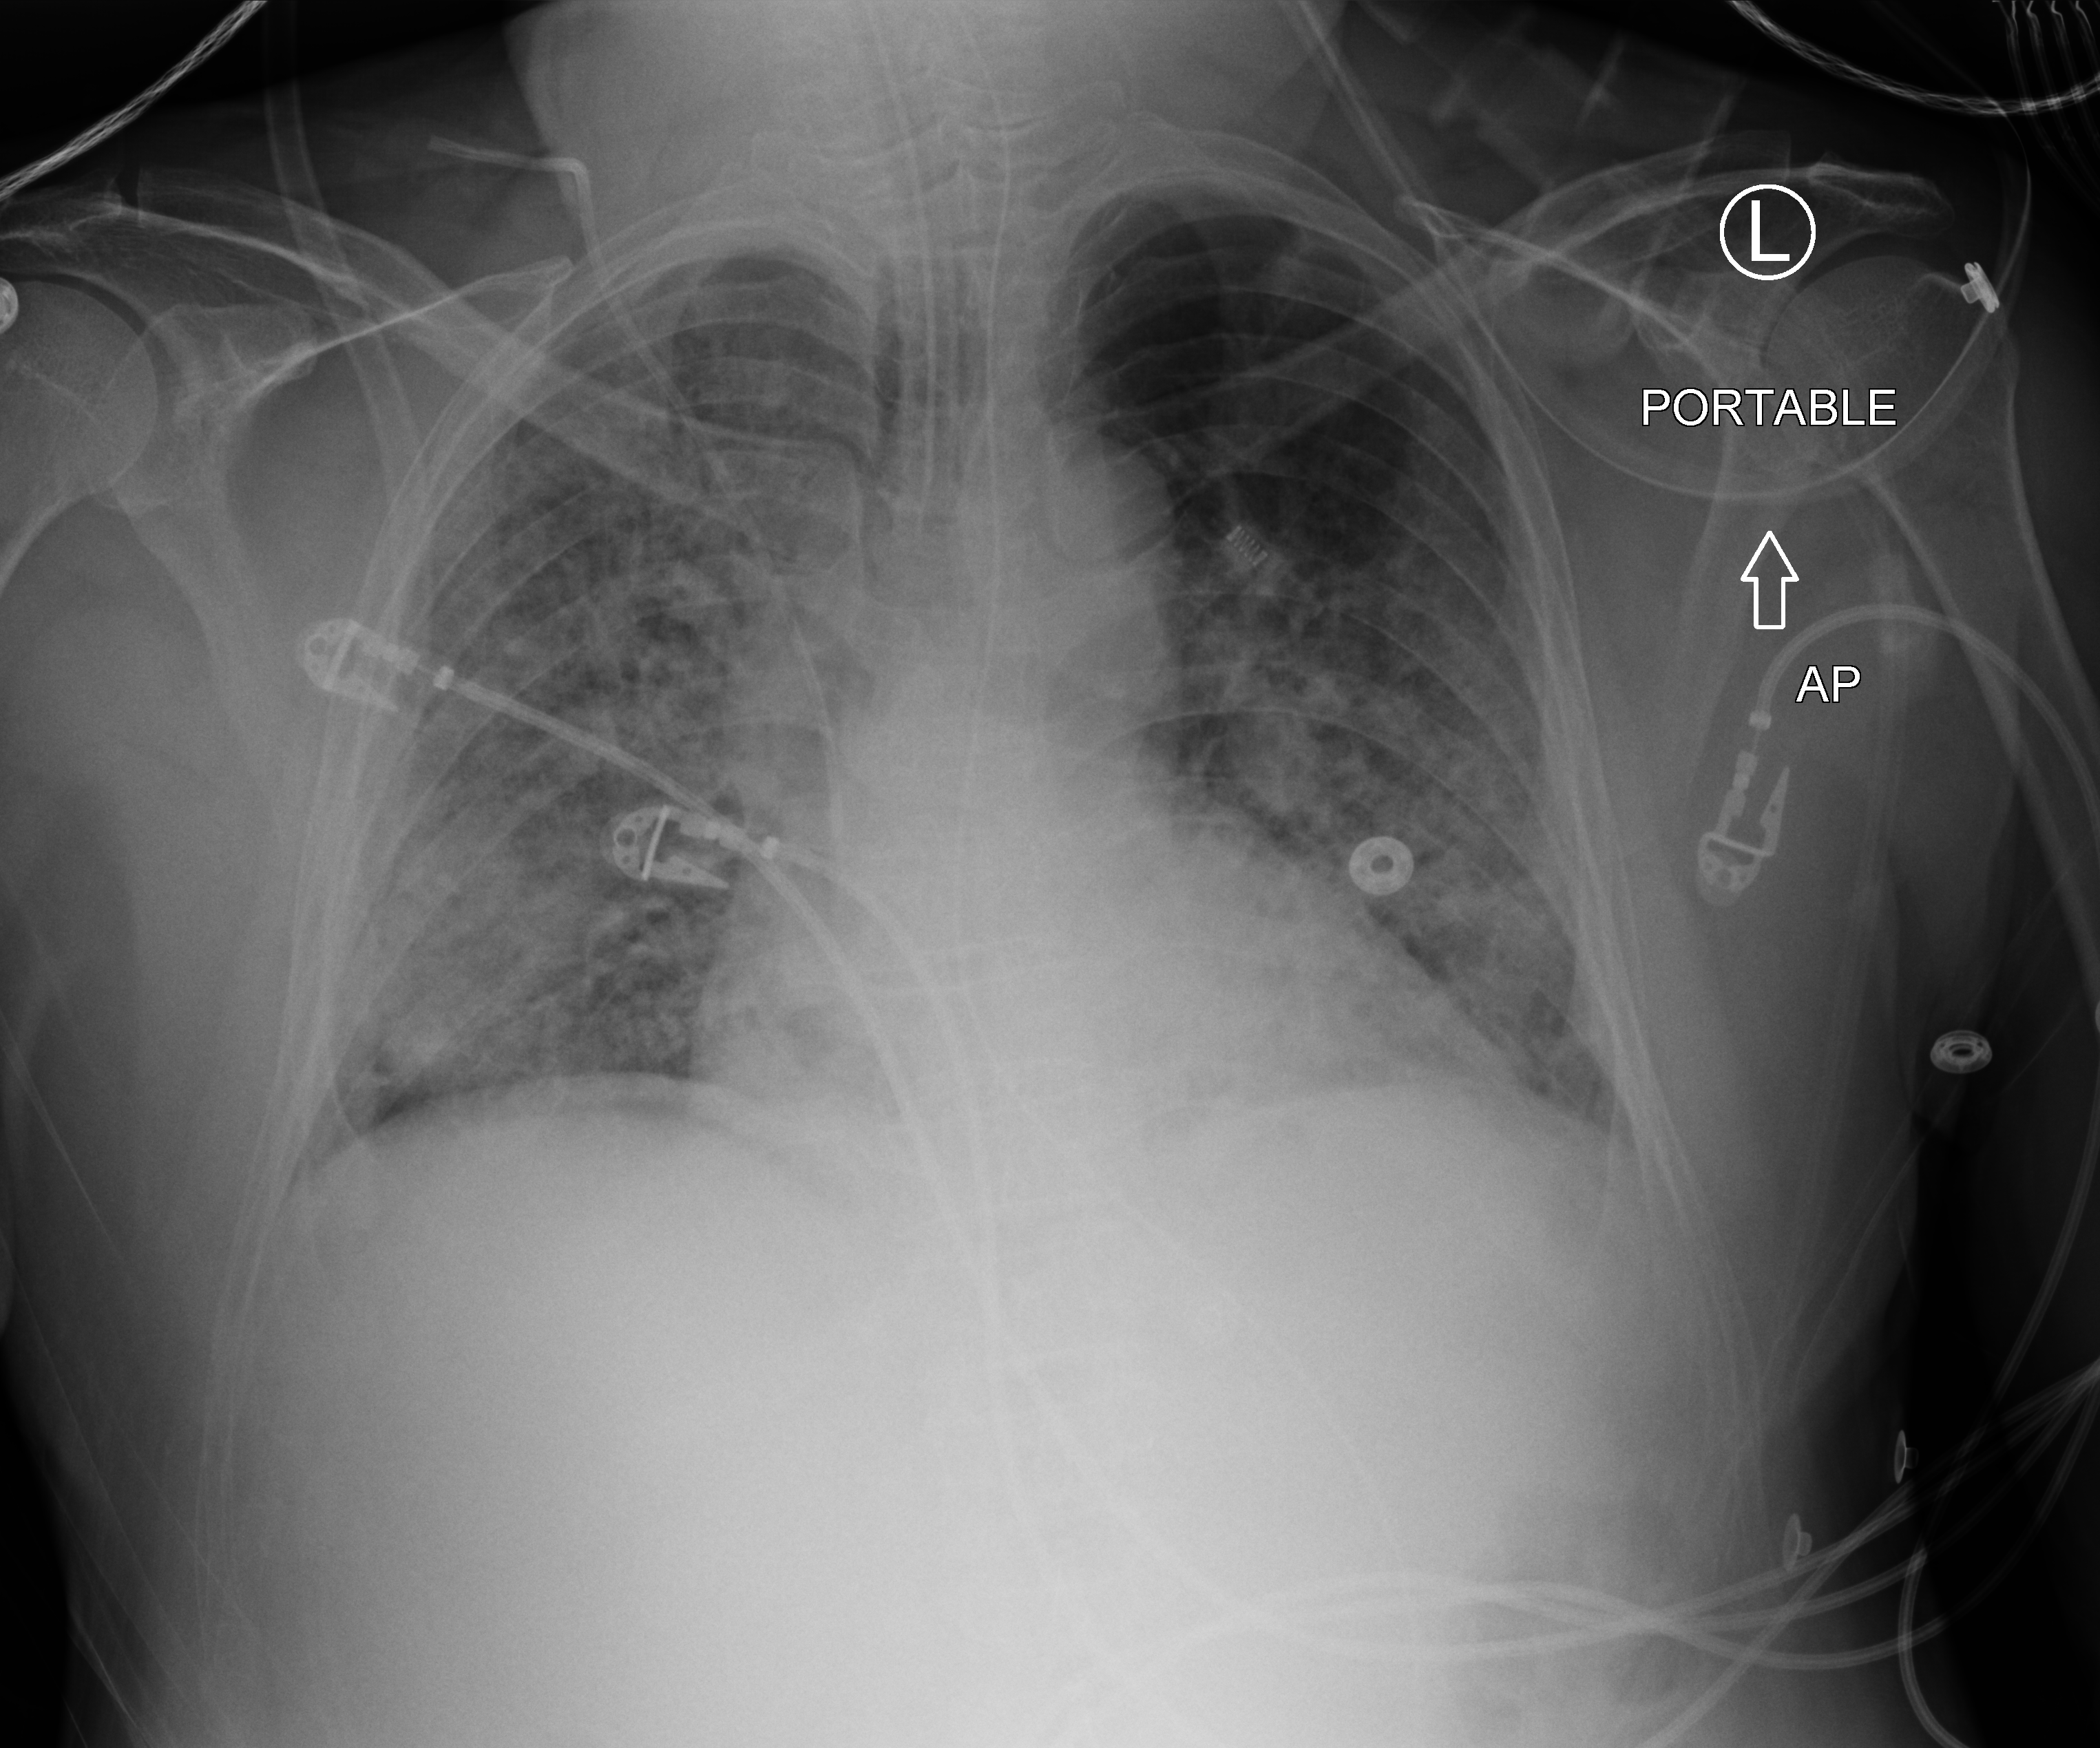
Bedside chest radiograph (computed radiography); anteroposterior (AP) projection. Patient hospitalised with COVID-19; male, aged 60–74 years.
From the hospital-stay record, not from the radiograph (when in the stay this image was taken is not recorded): mechanically ventilated during this hospital stay: yes.